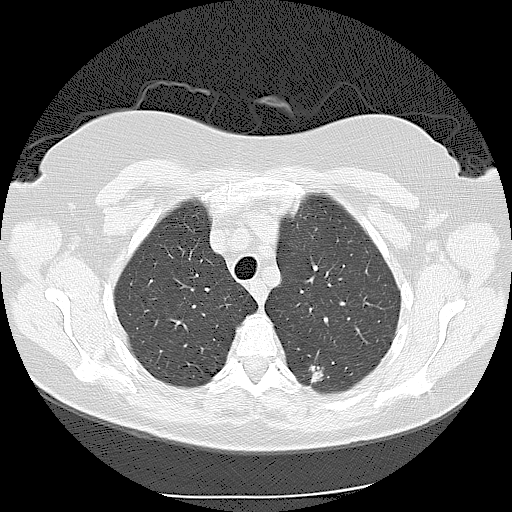
Chest CT (low-dose screening protocol), one axial image; second screening round (one year after baseline); lung window (W 1500 / L -600 HU); 2.5 mm slice thickness. Female, age 56 years at enrolment. Current smoker at enrolment.
• Lesion marked by an expert reader, bounding box [x1, y1, x2, y2] px = [290, 347, 347, 400].
• The exam's reader record, not a measurement of the box and not confirmed to be the same lesion: non-calcified nodule or mass ≥4 mm, left lower lobe, 9 × 9 mm, spiculated (stellate) margins, soft tissue attenuation, pre-existing on the prior screen: yes; interval growth: yes.
• Participant outcome: lung cancer diagnosed 173 days after this screen — adenocarcinoma, NOS, left lower lobe, moderately differentiated (G2), stage IIA (AJCC 6th edition), 15 mm at pathology.